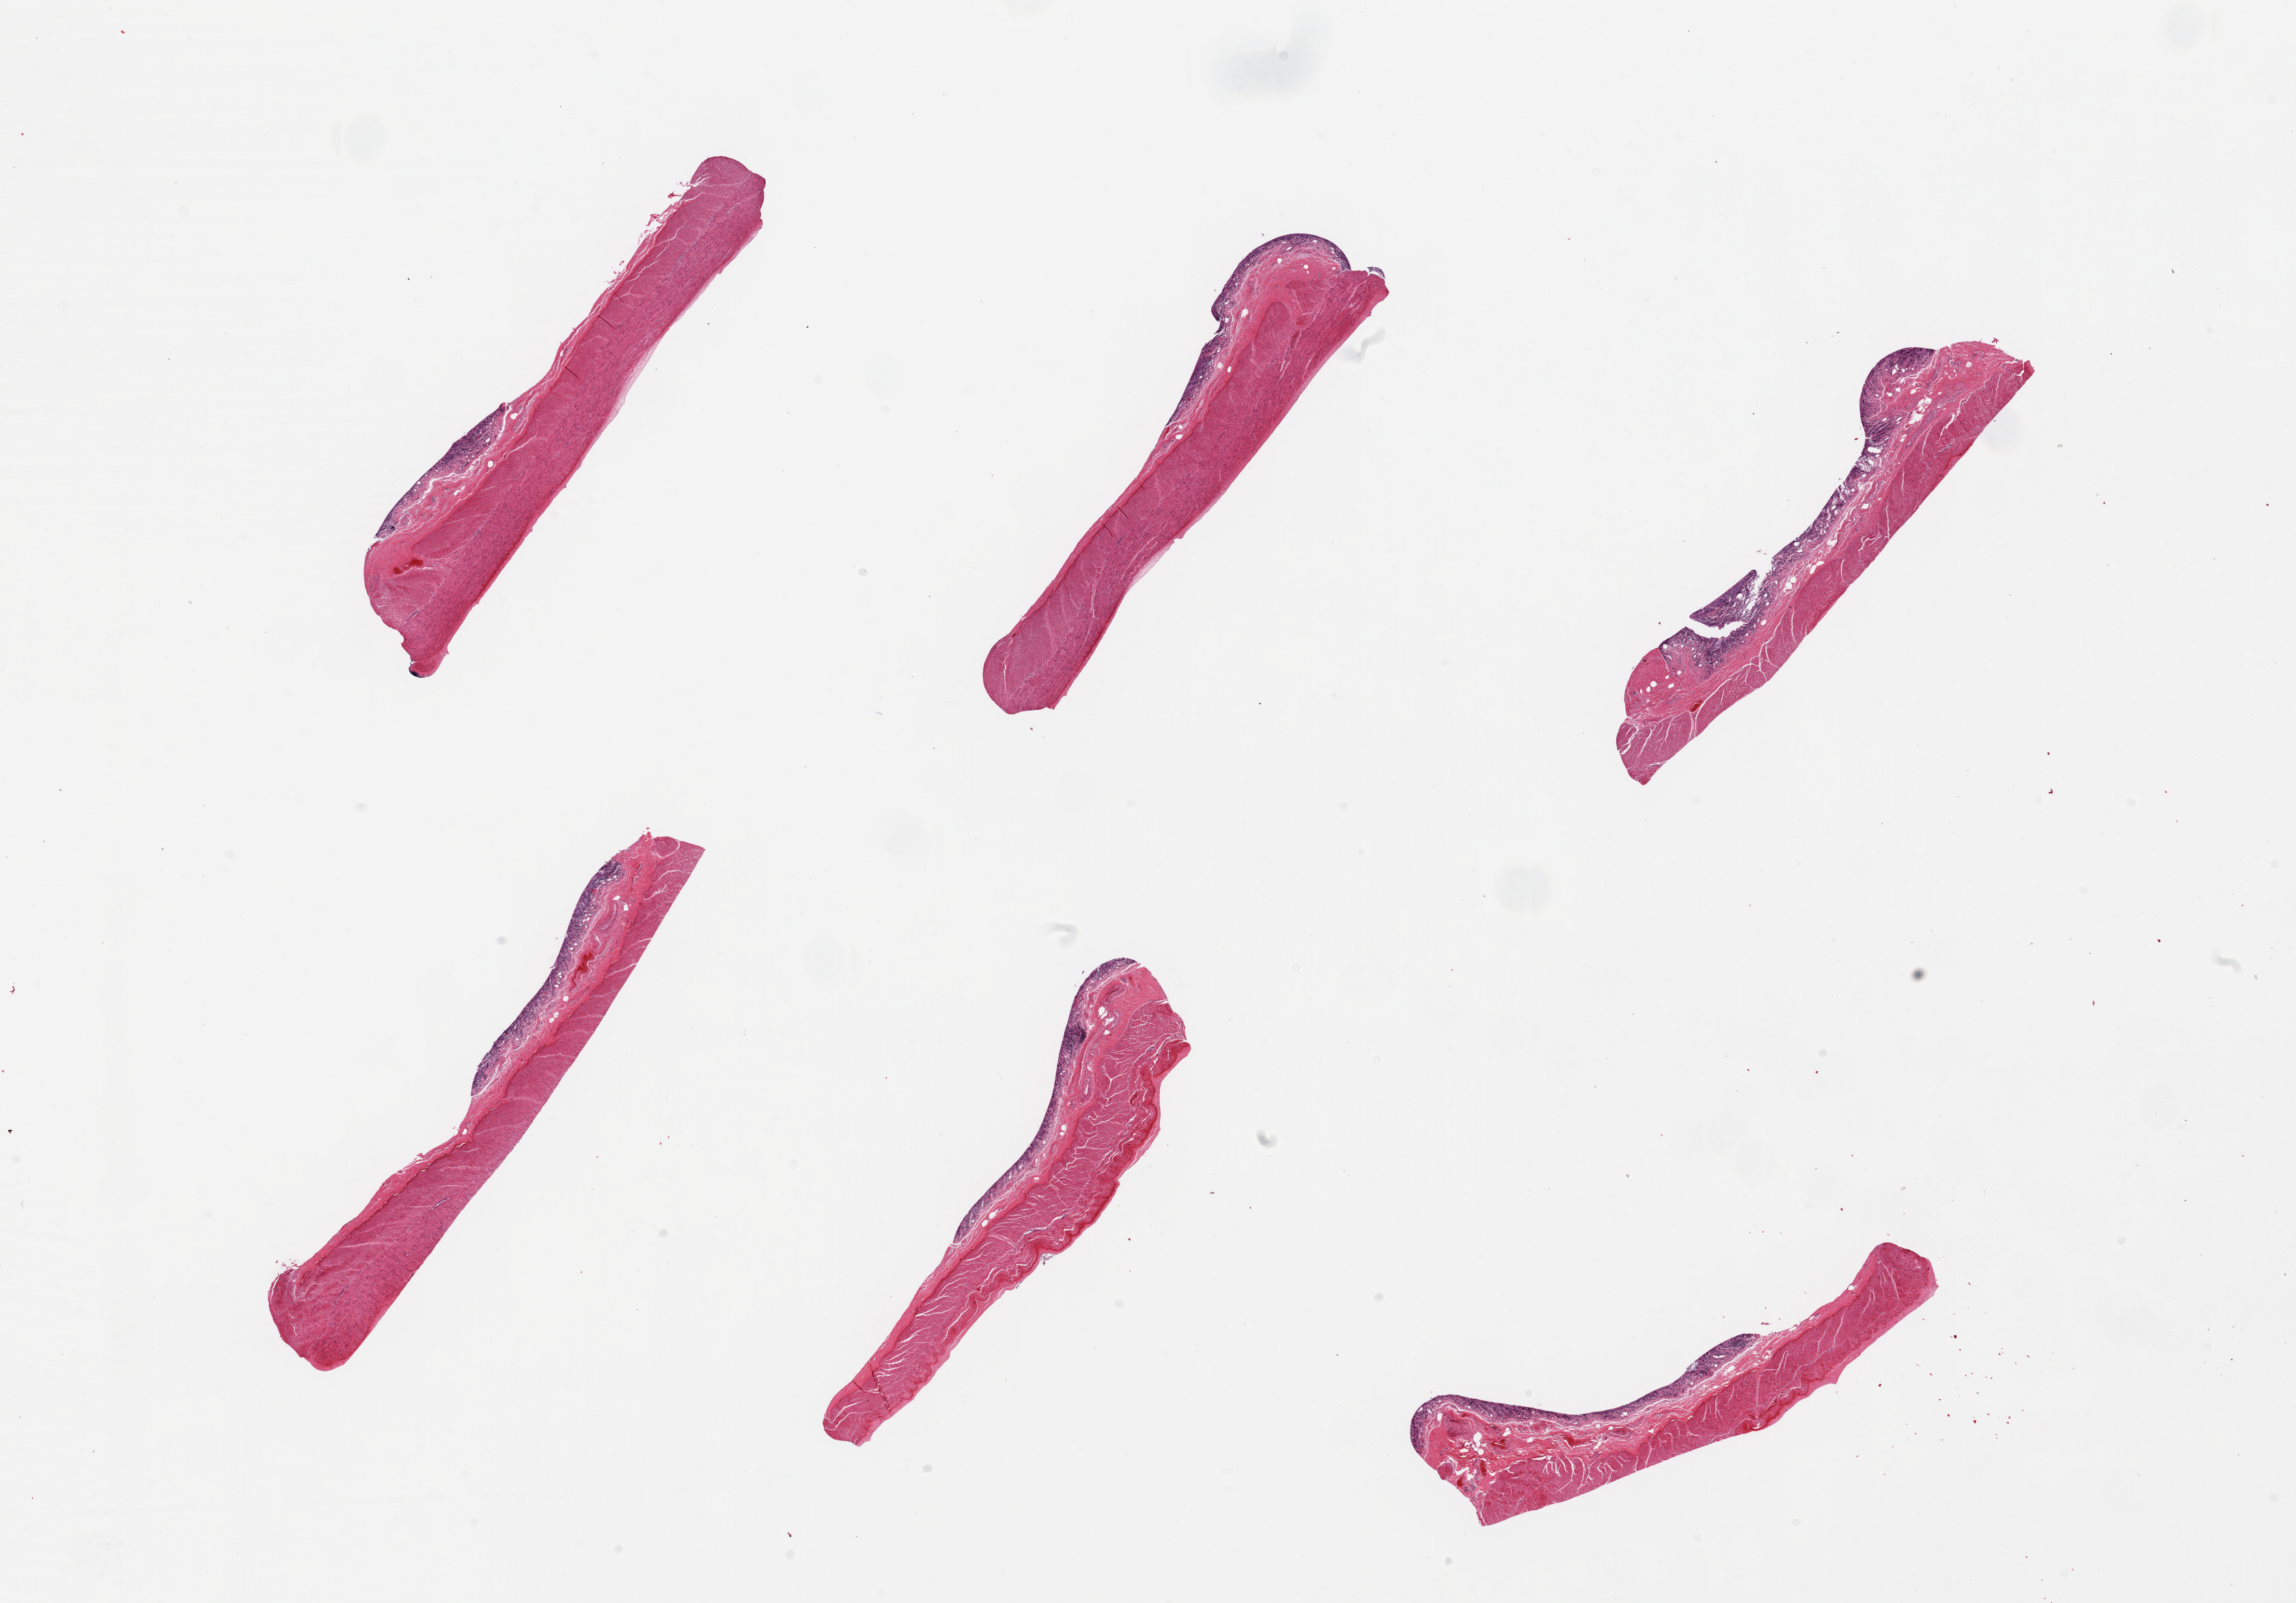
Whole-slide image, hematoxylin and eosin (H&E) stain, brightfield, low-resolution overview of the scanned area, about 26.6 x 18.6 mm (from a 20x scan); PAXgene-fixed paraffin-embedded (PFPE) section; section of transverse colon (target tissue); donor tissue sample.
* review note (as recorded): 6 pieces; autolyzed mucosa; preserved muscularis